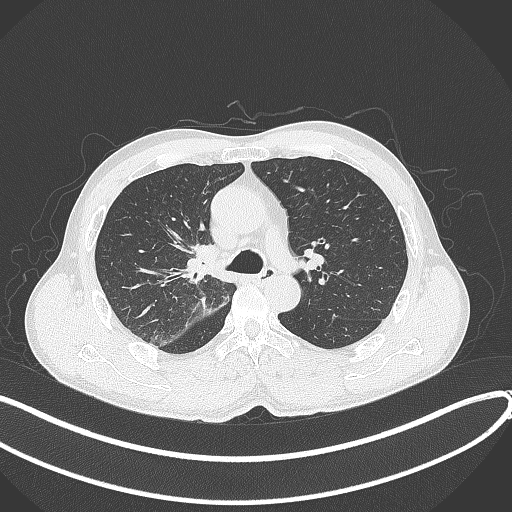
Chest CT, one axial slice; position 258 of 409 along the scan axis; lung window (W 1500 / L -600 HU); 1 mm slice thickness; 512 × 512 image matrix, field of view 400 × 400 mm. Male patient, age 53 years. From the clinical record (not read from this slice): clinical TNM (as recorded): T1b N0 M0.
Structures marked on this image (rectangle marked by the reading radiologist):
- lung tumour (recorded histology: squamous cell carcinoma): bounding box <177,239,224,287> (left, top, right, bottom; pixels)